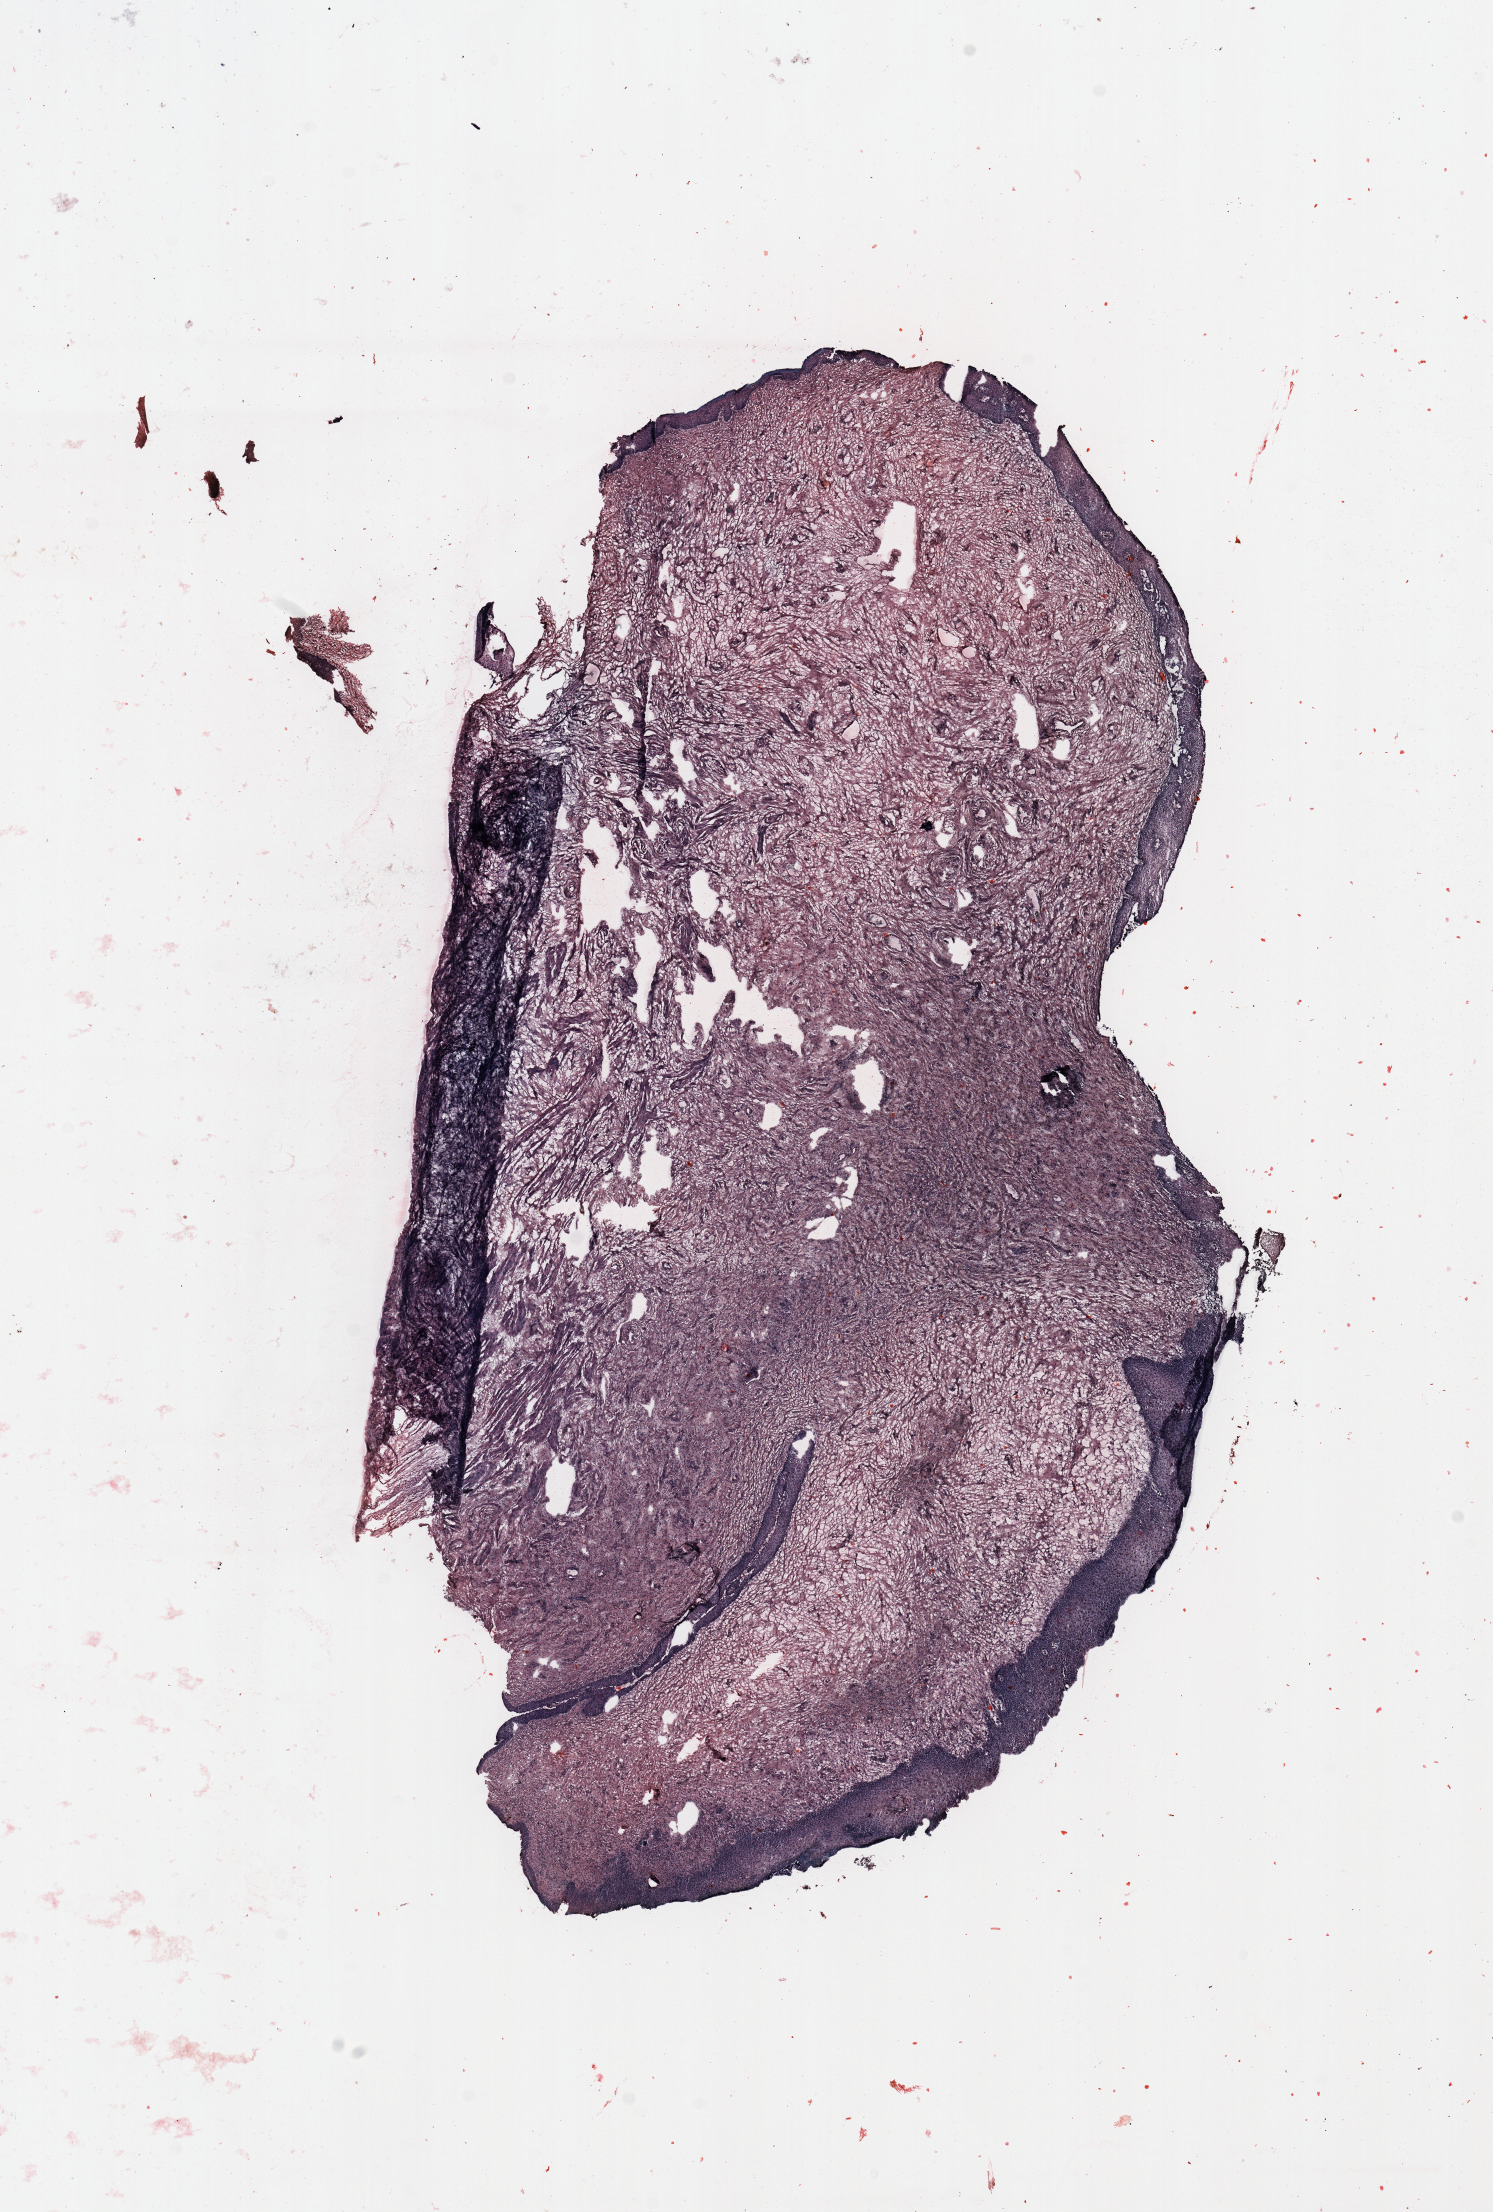
Digitized H&E tissue section (whole slide) — whole scanned area (about 11.8 x 17.5 mm, acquisition: 20x scan) shown as a low-resolution overview. Uterus, normal (non-tumour) tissue. Female, 60 y/o.
This section: normal (non-tumour) tissue from the same patient. Patient diagnosis: Endometrioid adenocarcinoma, NOS.